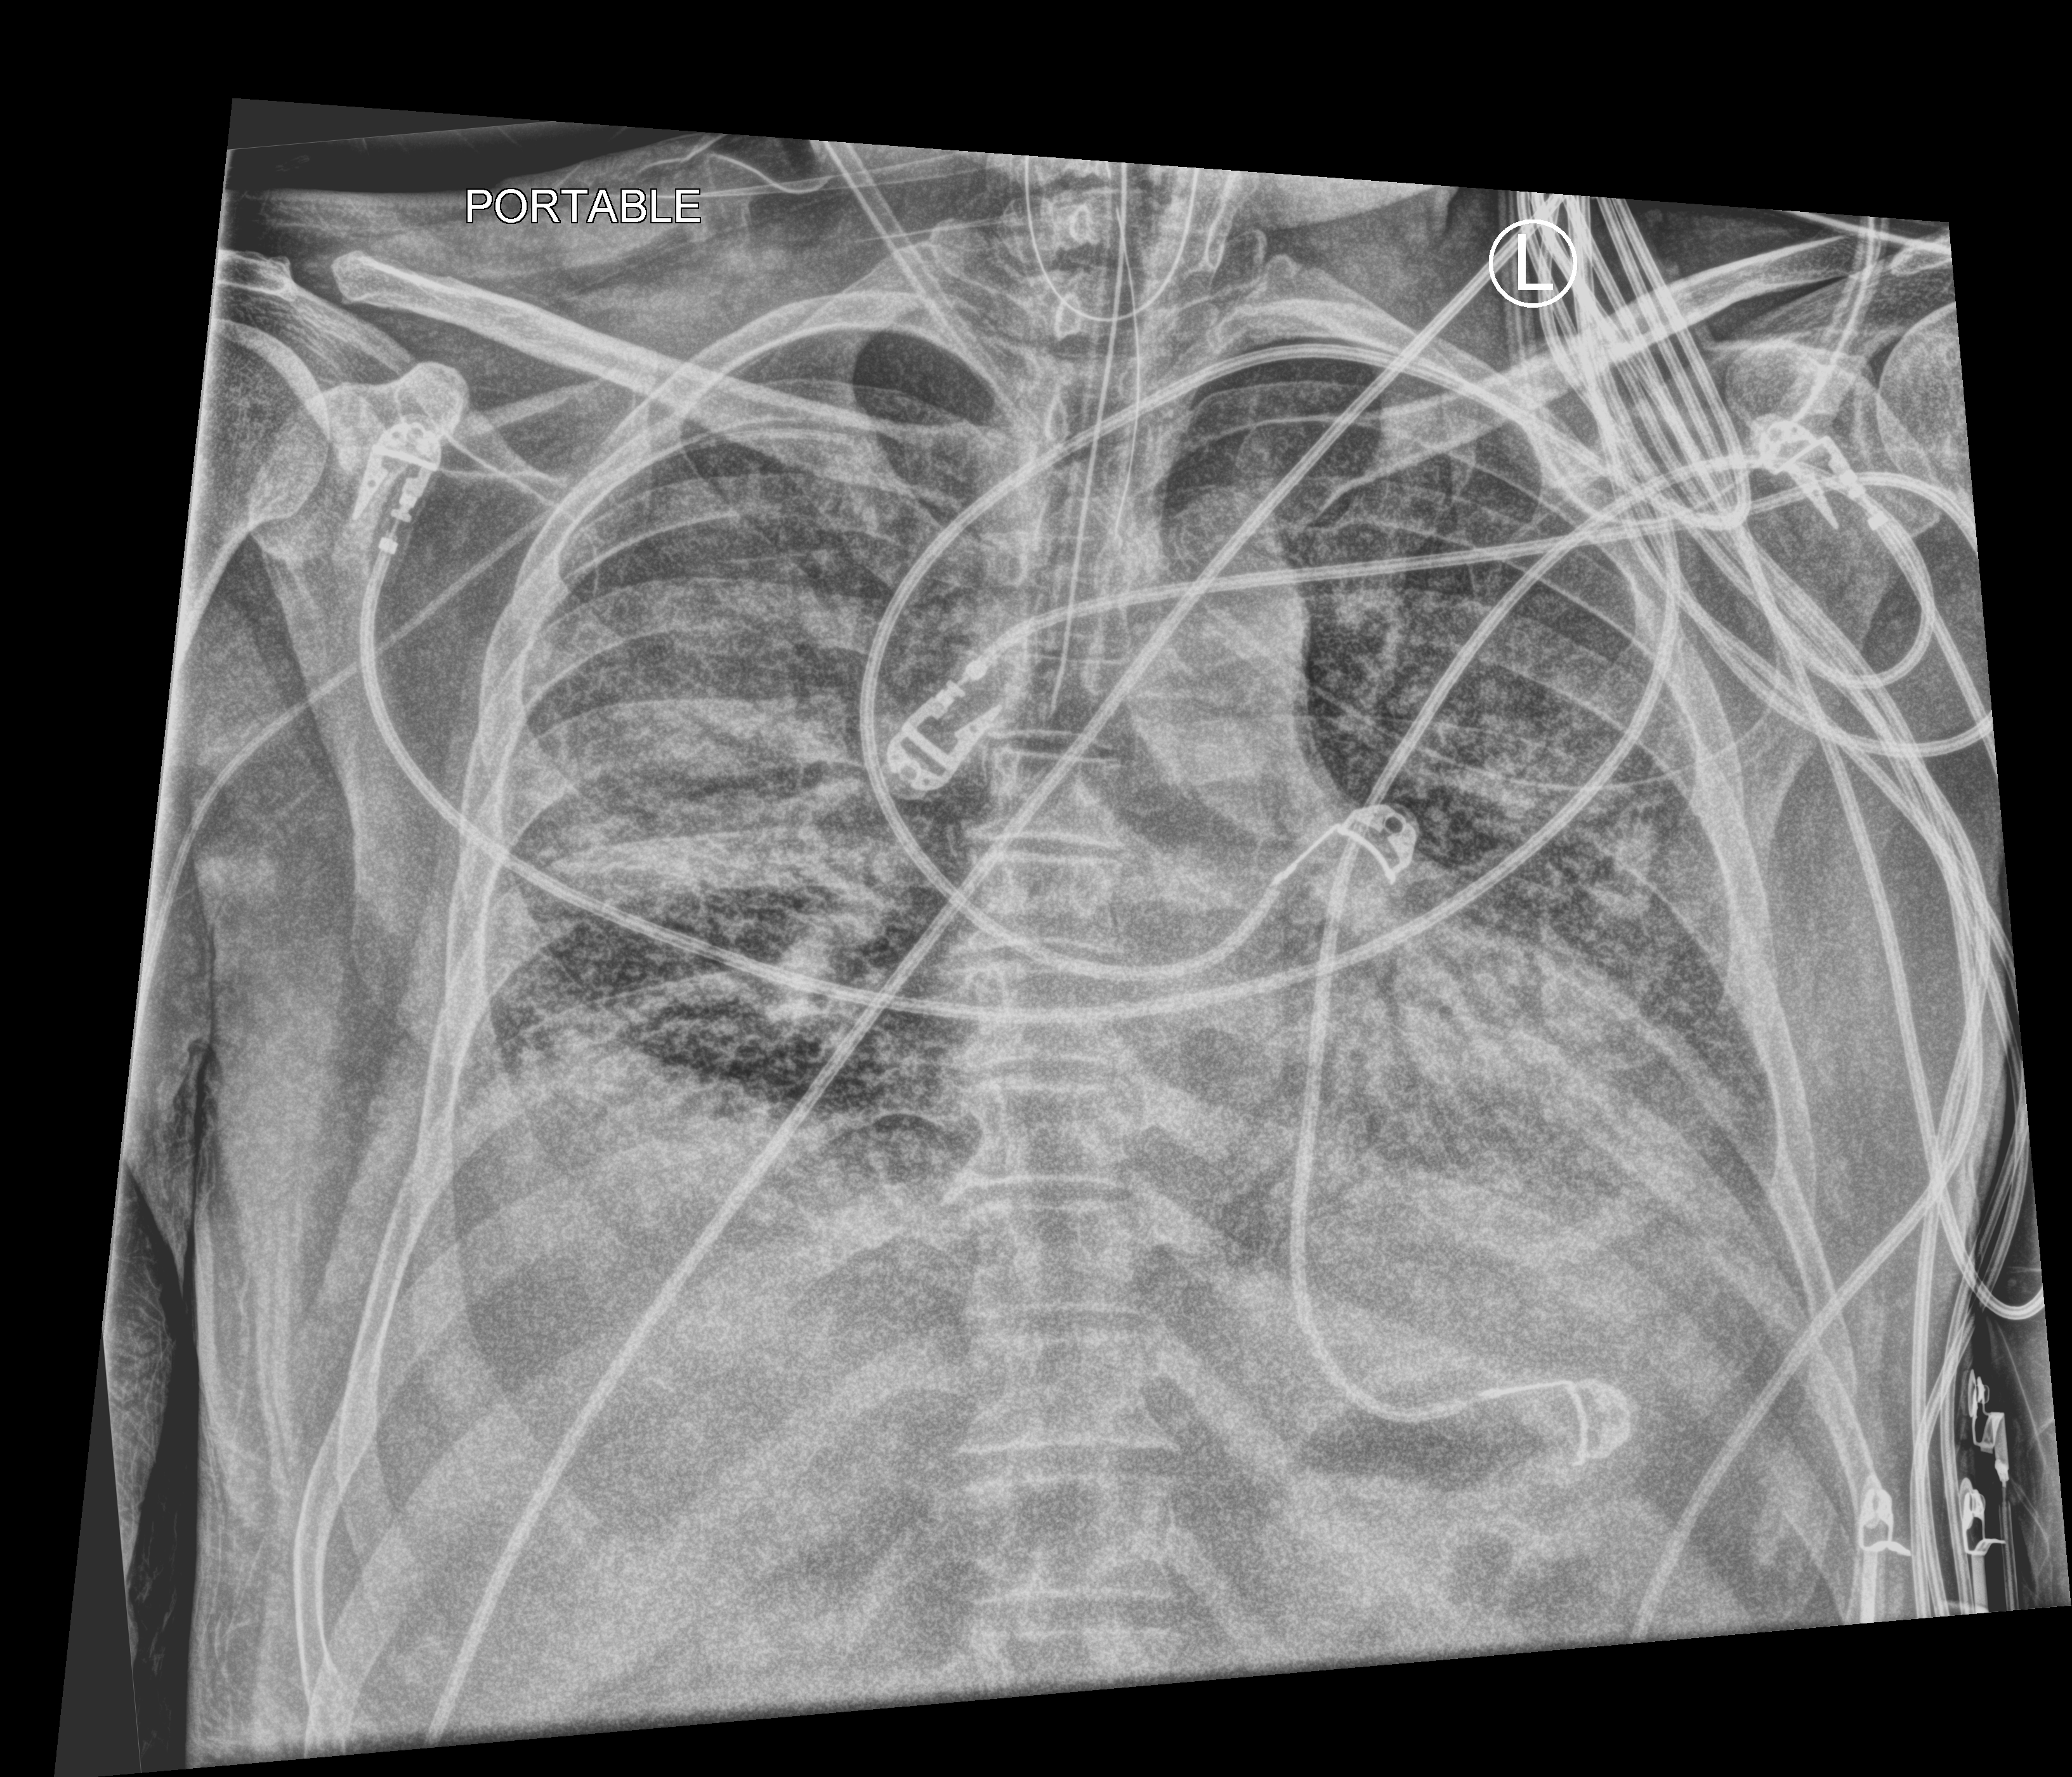
Bedside chest radiograph (computed radiography); anteroposterior (AP) projection. Patient hospitalised with COVID-19; male, aged 18–59 years.
Hospital-stay facts (about this admission, not read from this image; timing relative to this image not recorded): admitted to intensive care during this hospital stay: yes; mechanically ventilated during this hospital stay: yes; hypertension (admission record): no.